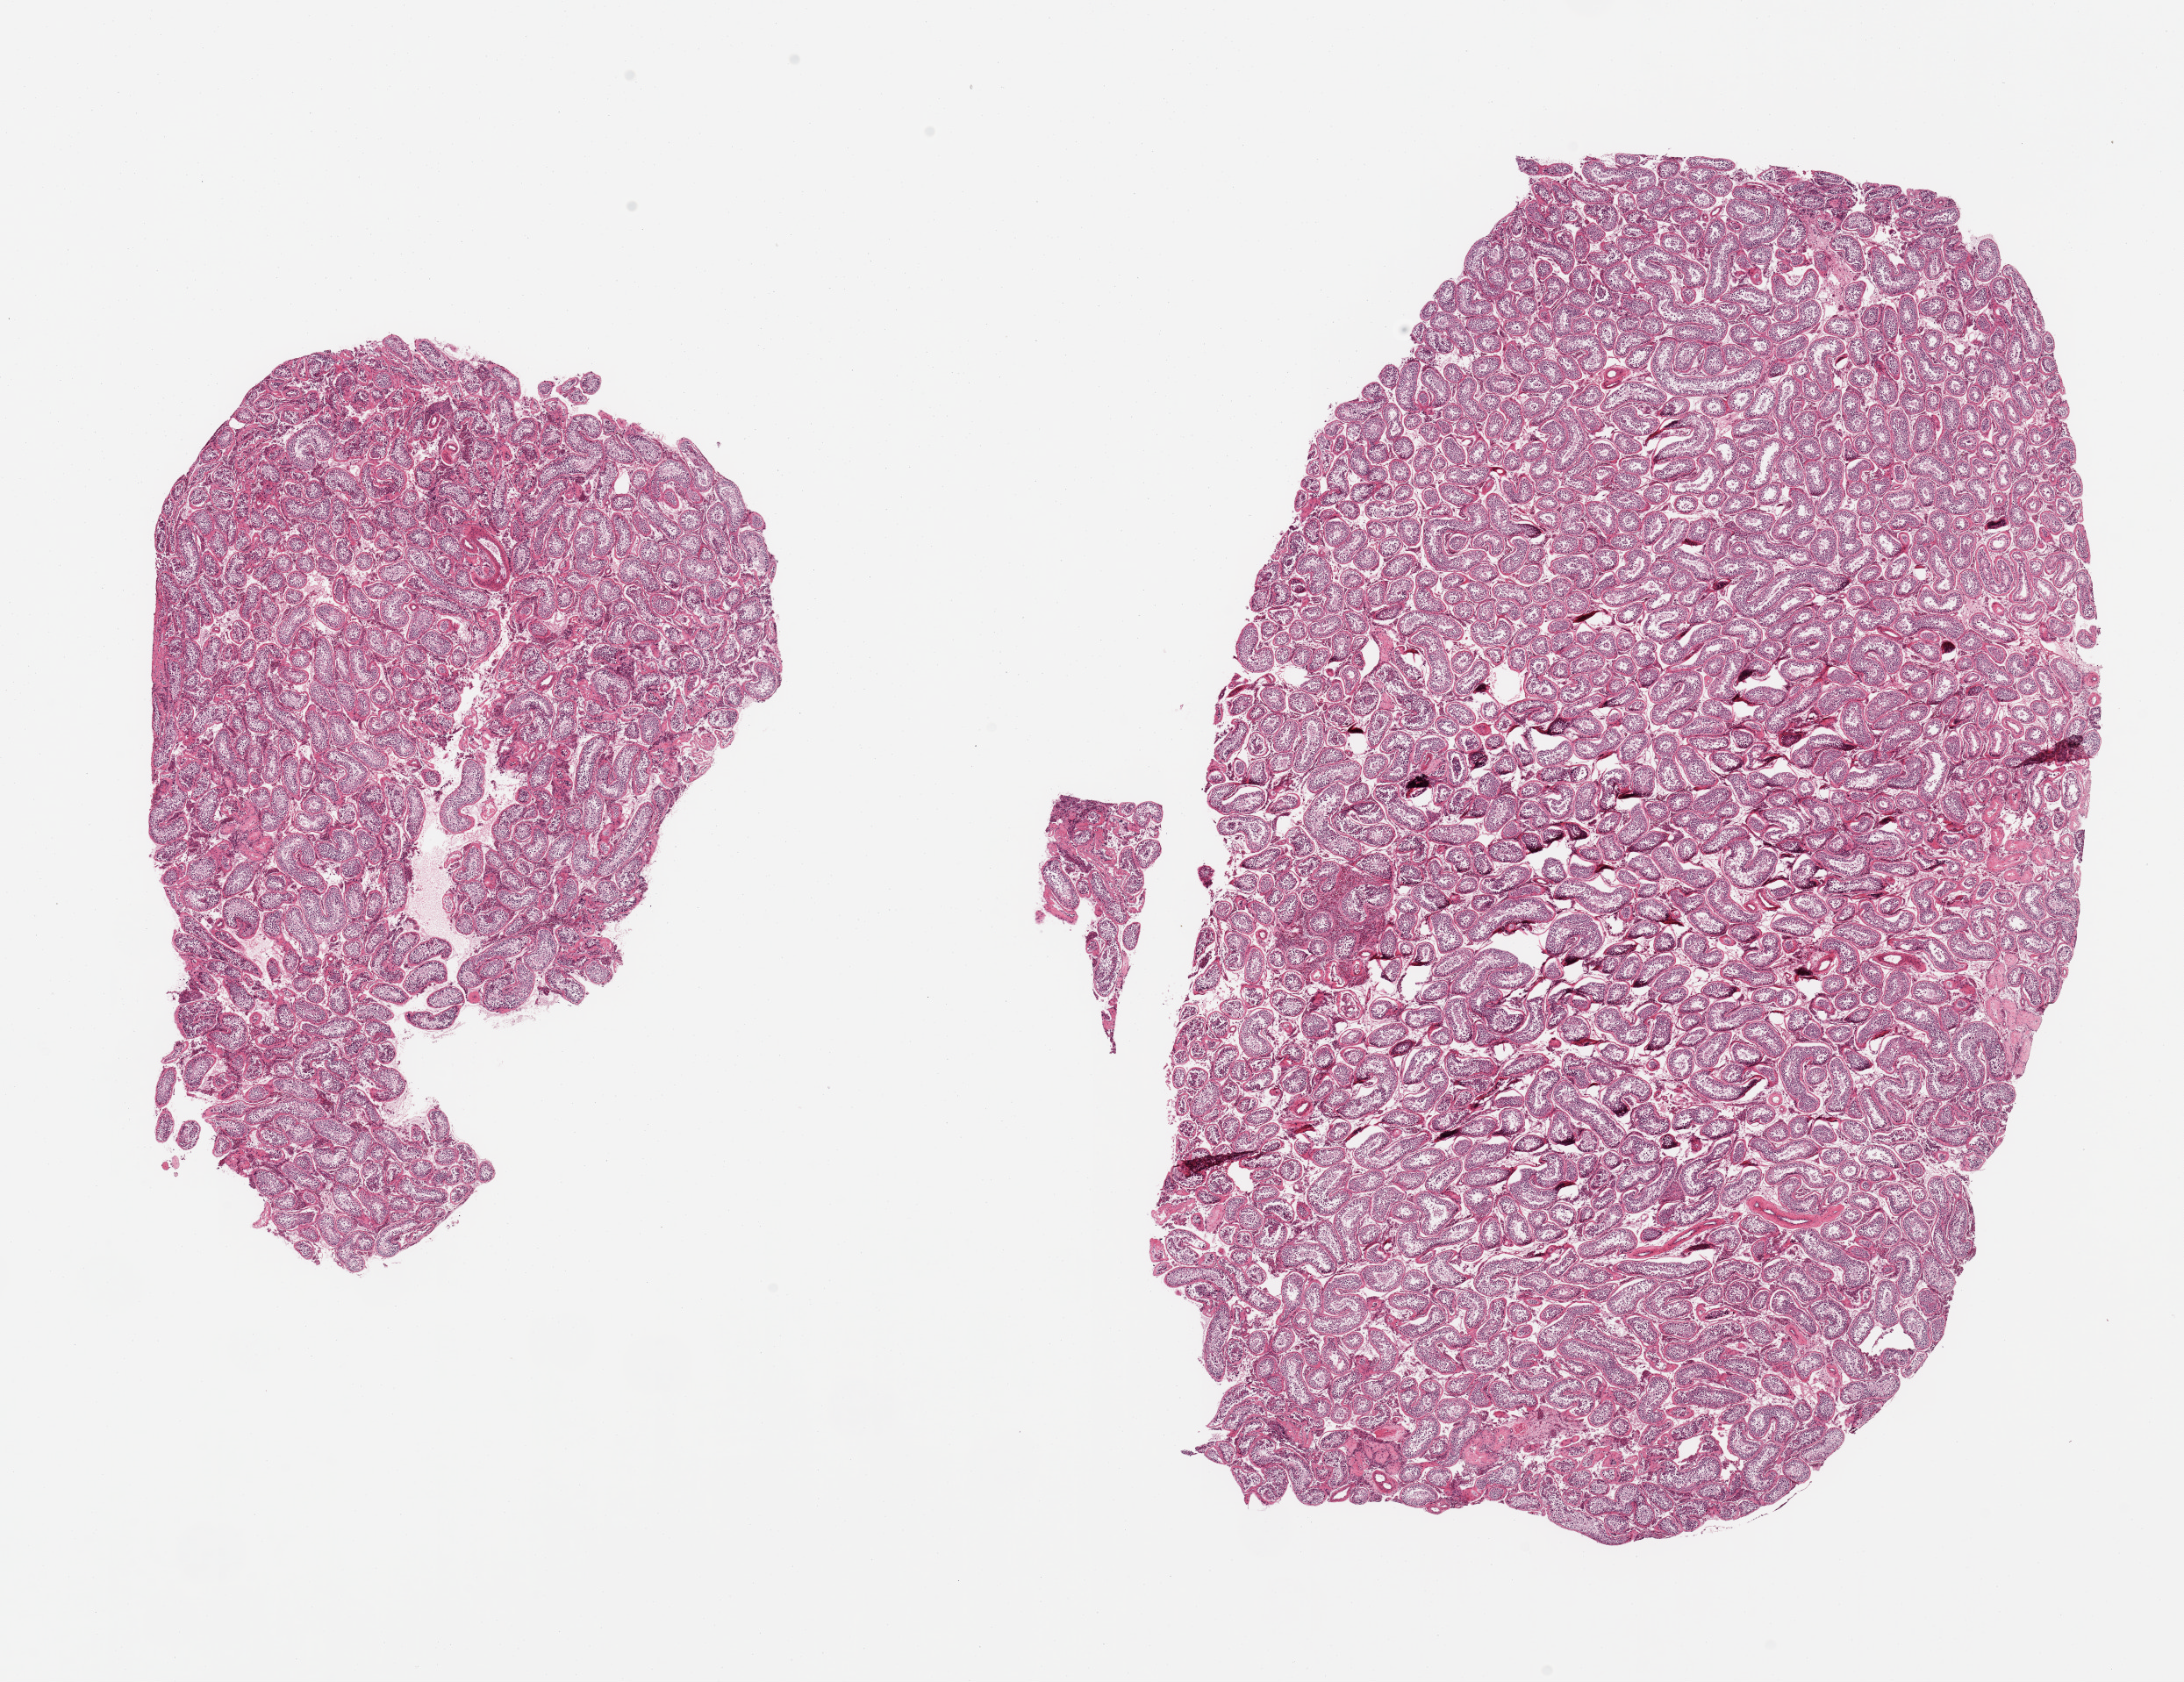
Whole-slide image, haematoxylin and eosin stain, brightfield — shown as a low-resolution overview of the whole scanned area (about 19.7 x 15.2 mm, from a 20x scan); PAXgene-fixed paraffin-embedded (PFPE) section; target tissue: testis; donor tissue sample. Donor: male.
Reviewer comment on this tissue sample: 2 pieces, spermatogenesis is present.